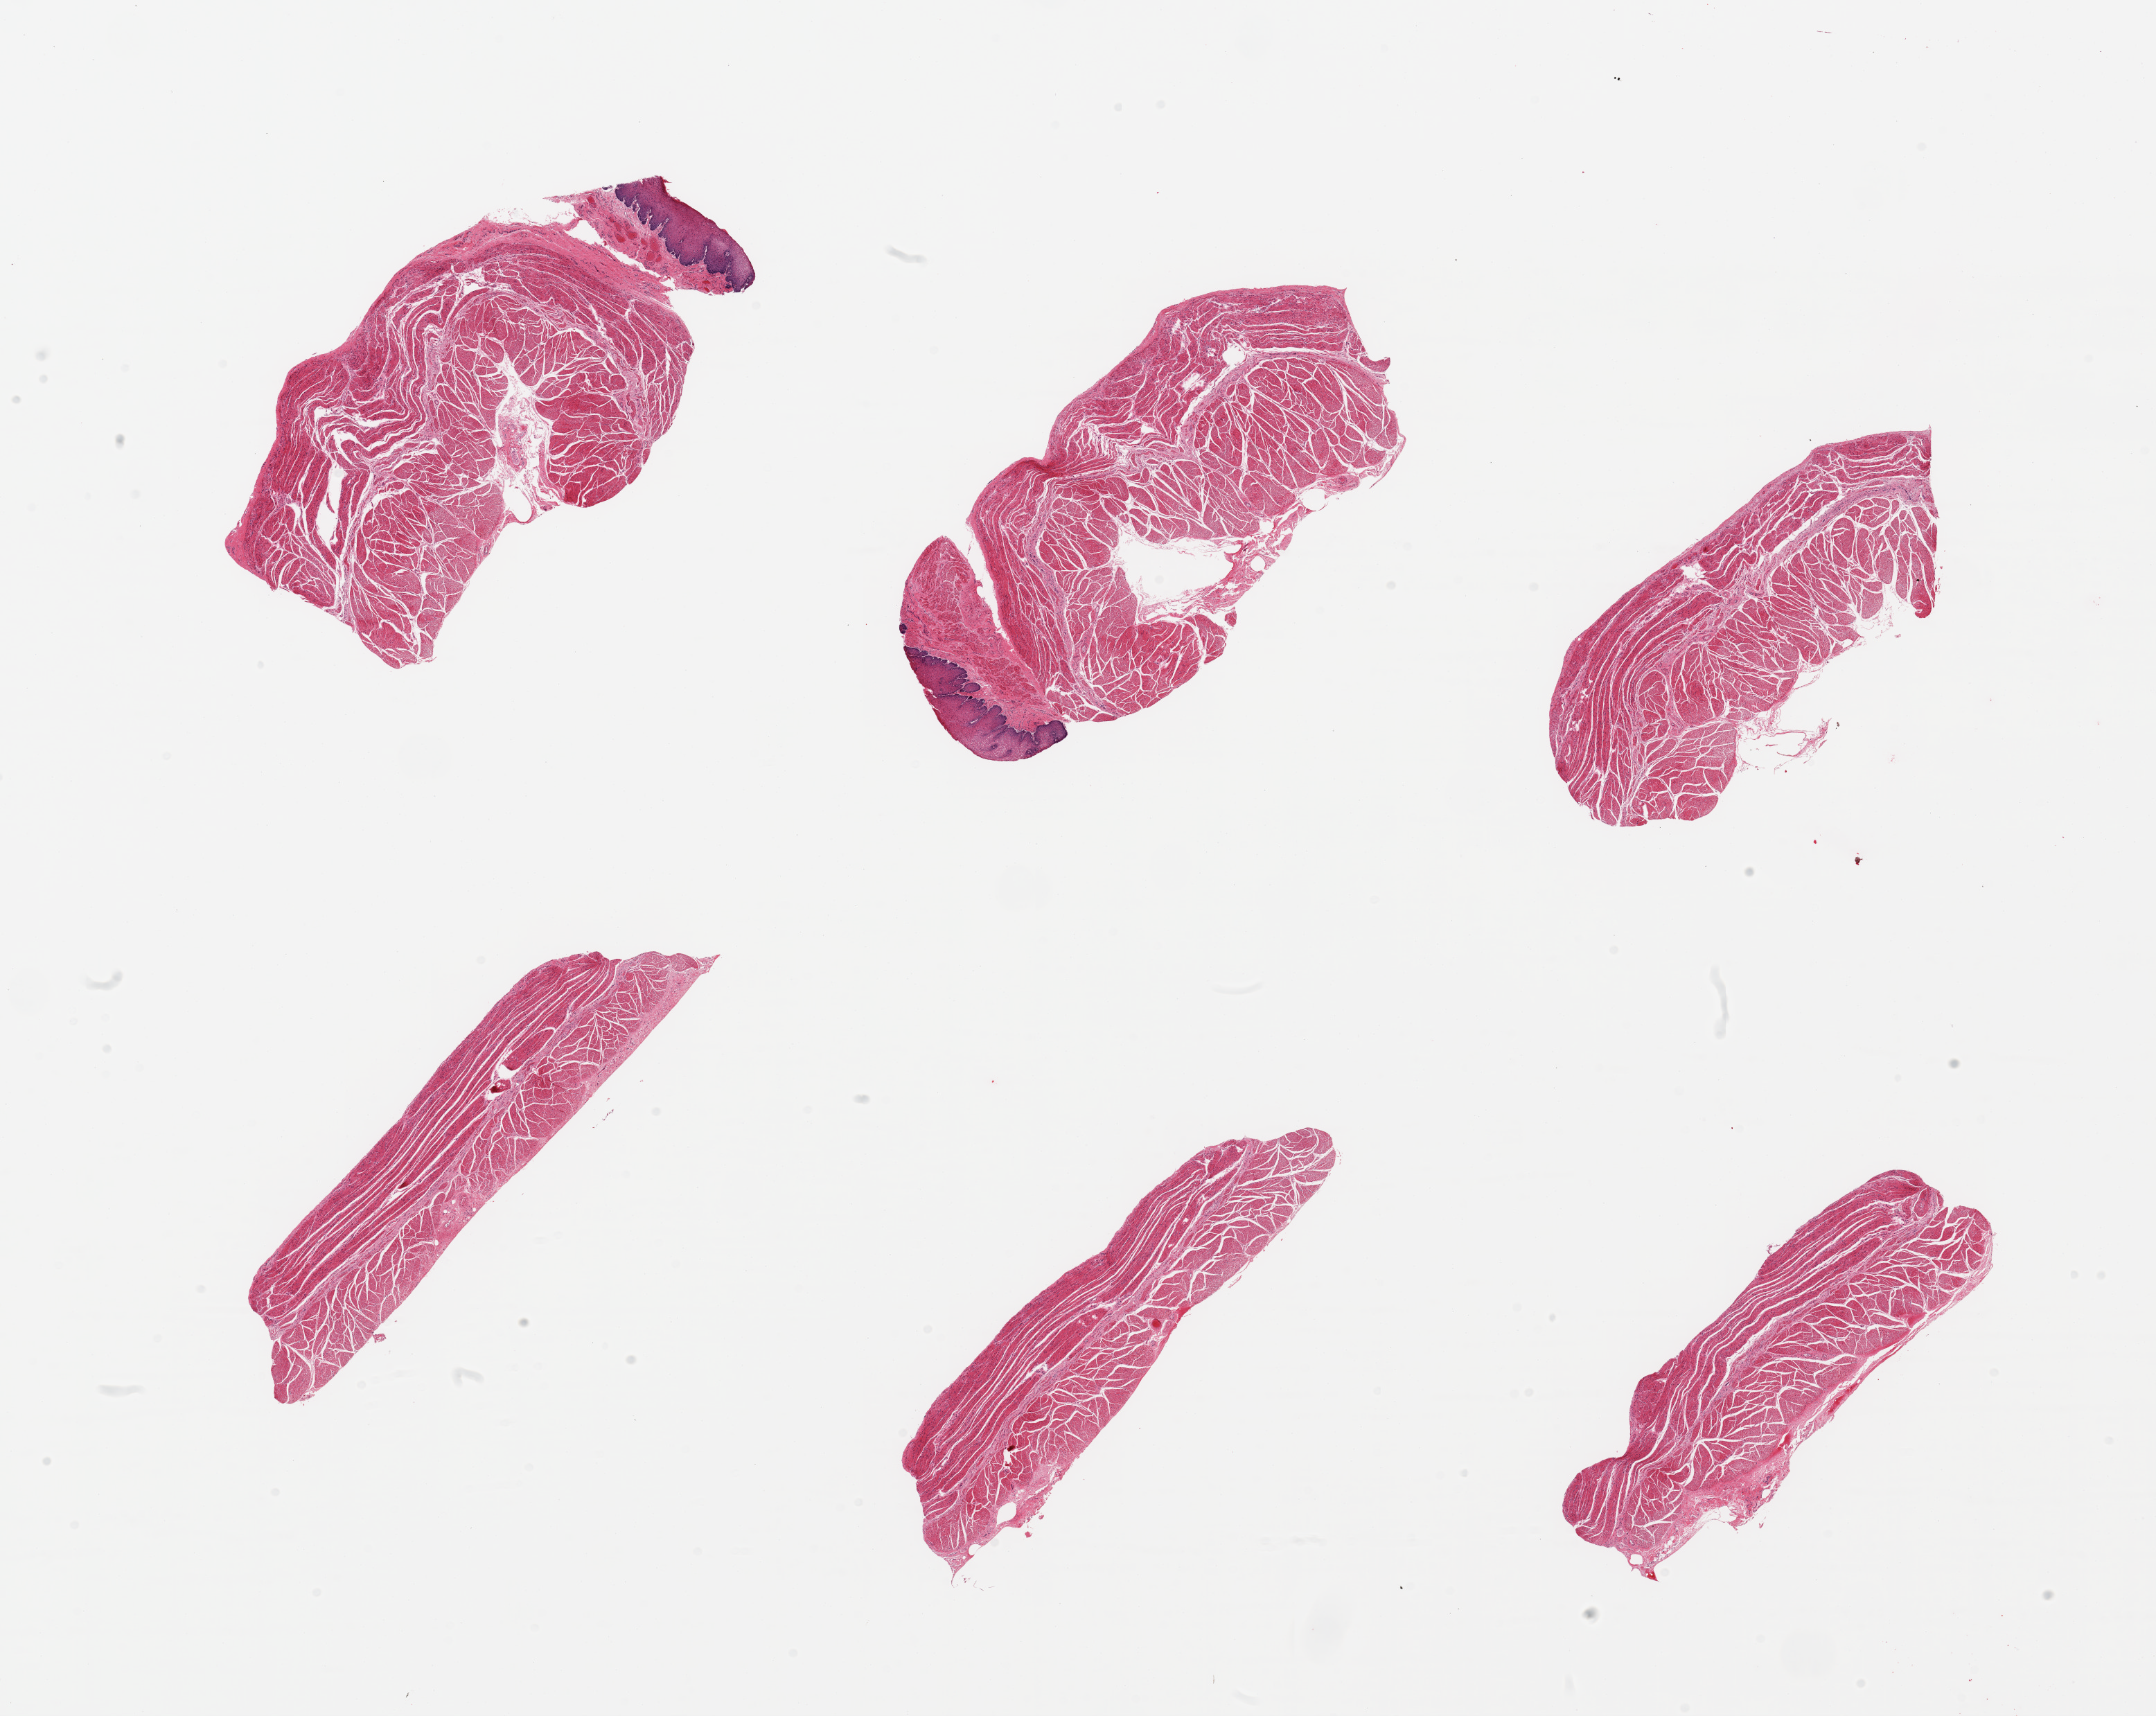
Digitized H&E-stained section — shown as a low-resolution overview of the whole scanned area (about 24.6 x 19.6 mm, from a 20x scan). PAXgene-fixed paraffin-embedded (PFPE) section. Section of esophageal muscle (target tissue). Tissue donor sample. Donor: male.
- review note (as recorded): 6 pieces trace 'contaminant' squamous mcuosa